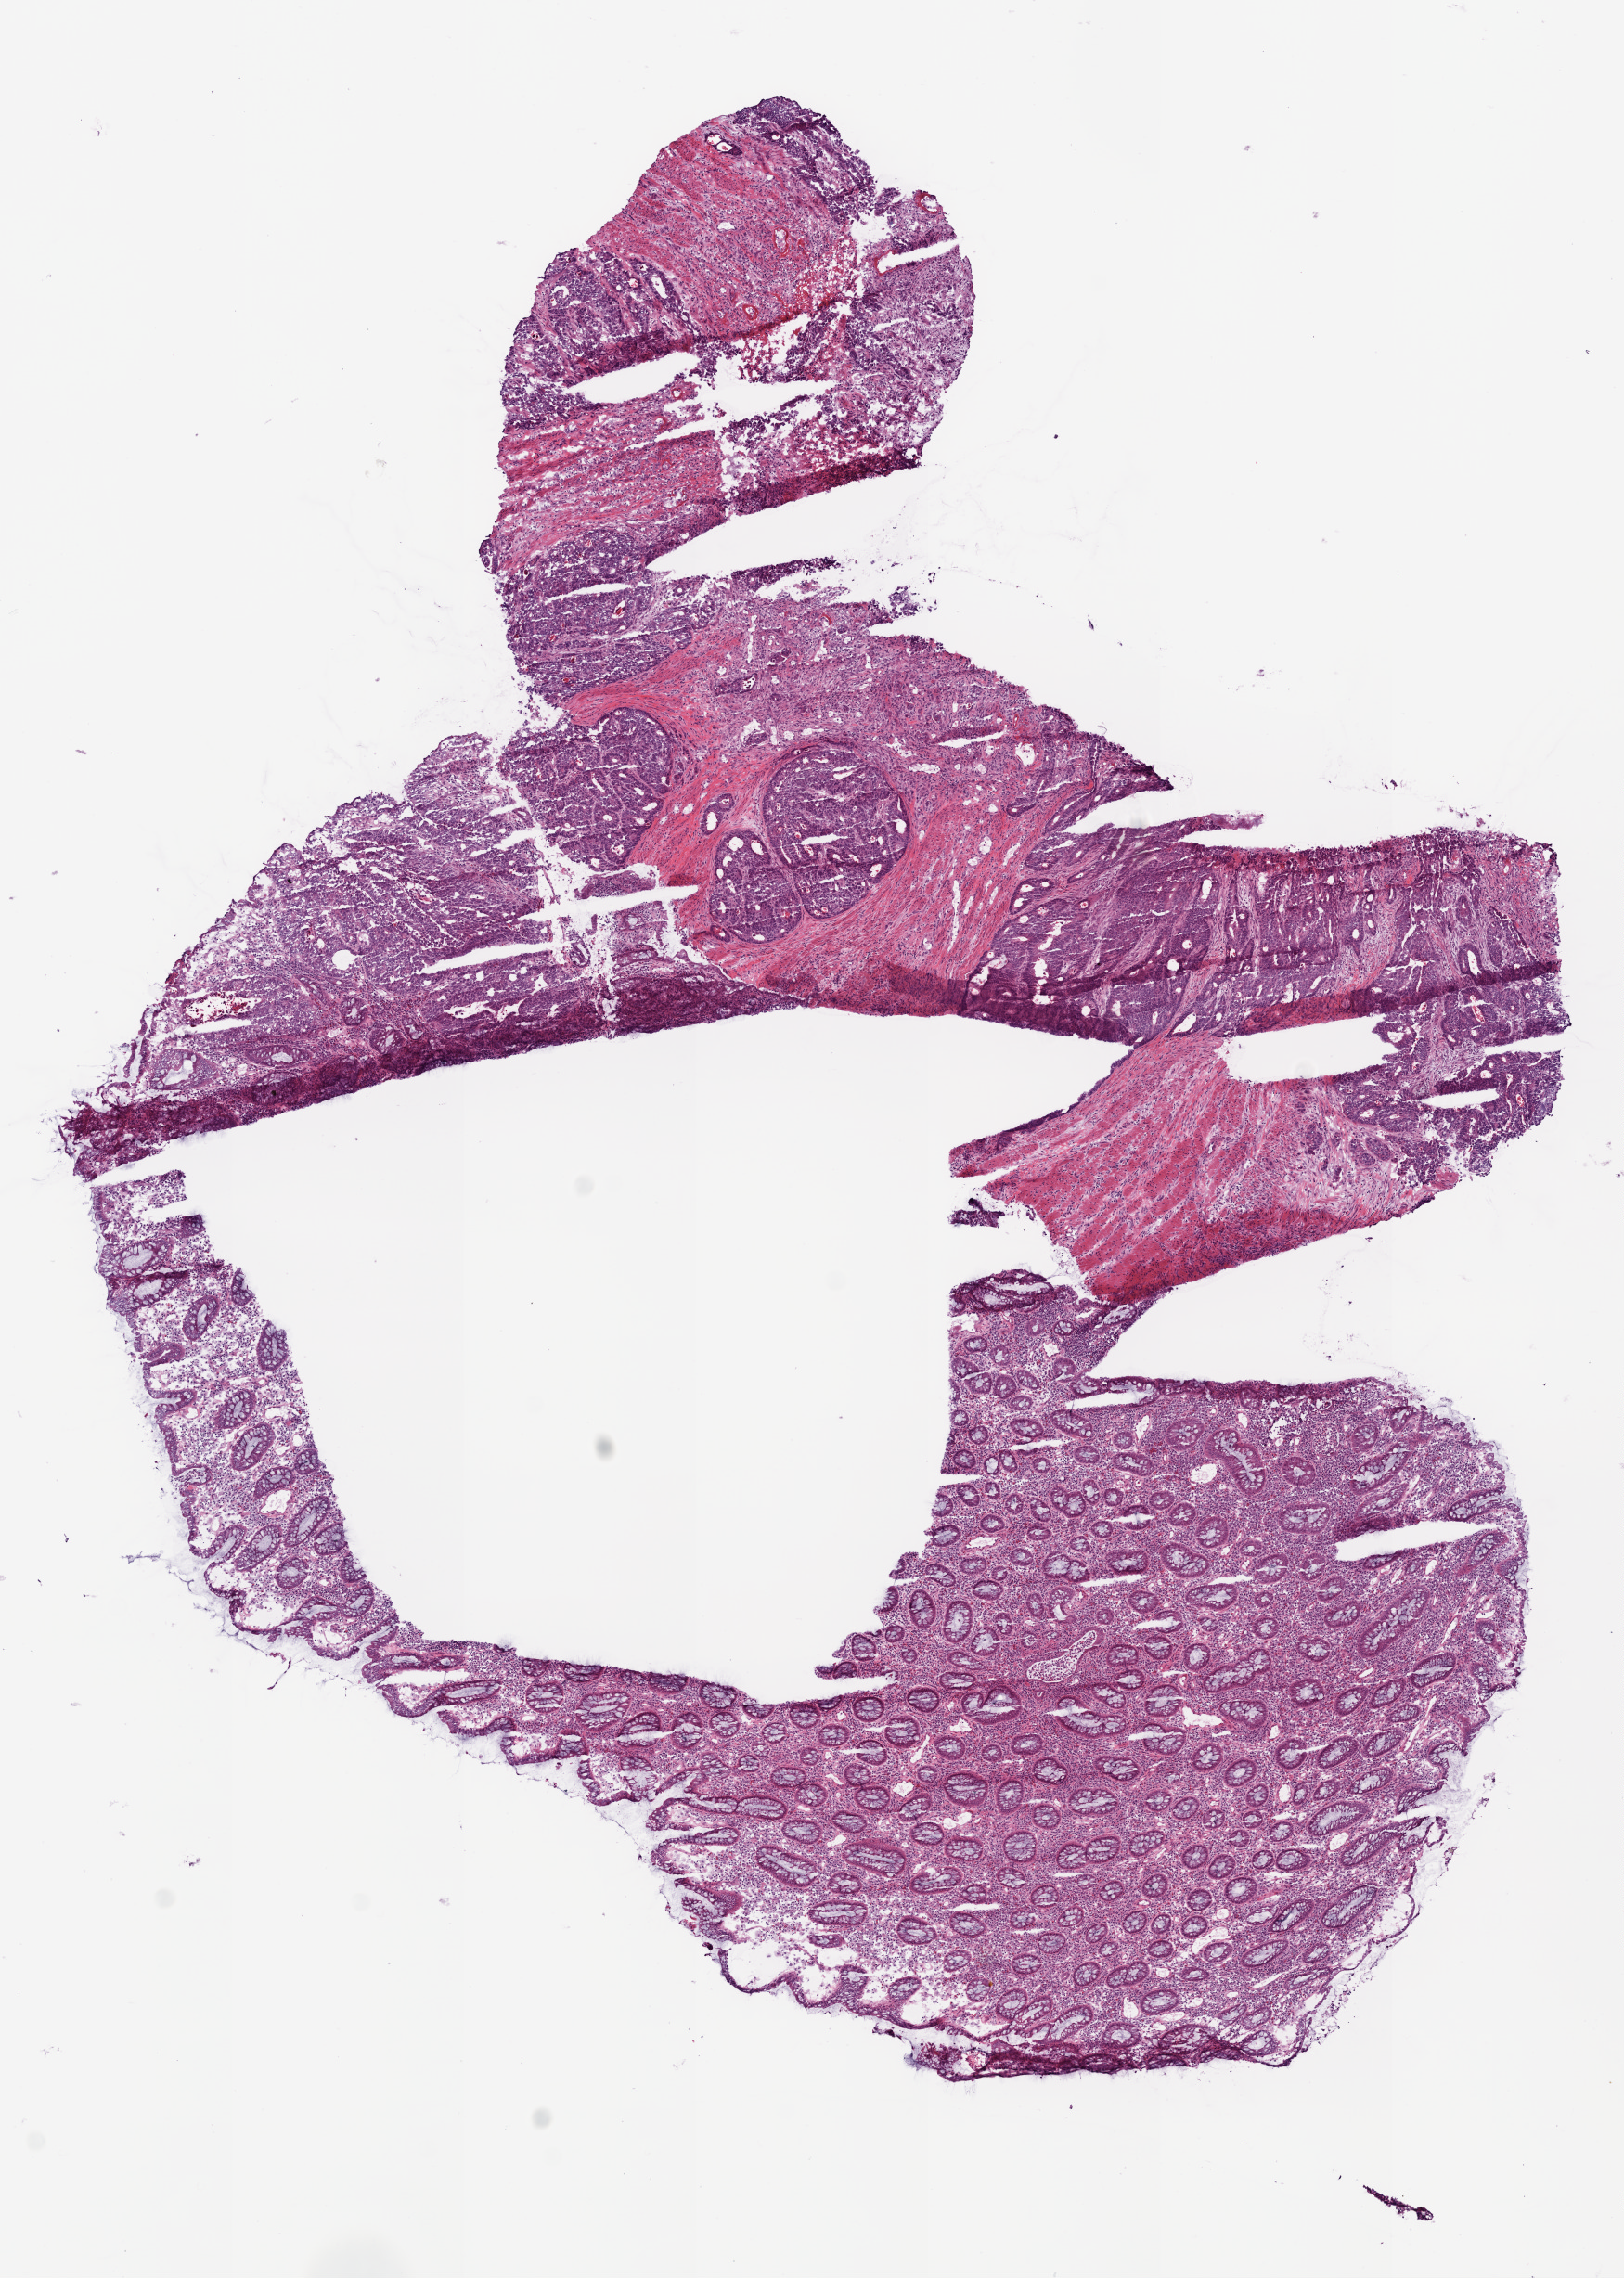
Whole-slide histology image, H&E, low-resolution overview of the scanned area, about 7.0 x 9.8 mm (acquisition: 20x scan), frozen section, primary tumour sample from the rectum. Male patient; age at initial diagnosis 77 years. Slide review estimates, as recorded: tumour cells 24%, tumour nuclei 25%, normal cells 70%, stromal cells 3%, necrosis 3%.
AJCC pathologic stage: IVA (7th edition). Pathologic diagnosis: Adenocarcinoma, NOS. Lymph nodes positive (case pathology): 21 of 34 examined.